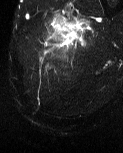
MRI of an extremity soft-tissue mass, one axial slice; position 10 of 60 along the scan axis; T2-weighted fat-saturated; MR volume resampled by the dataset authors to the PET/CT grid (not the native acquisition matrix); 3.27 mm slice thickness; 123 × 153 image matrix, field of view 120 × 149 mm. Male patient. Case-level facts recorded for this patient, not image findings: histological type: pleiomorphic liposarcoma; grade: high; site of the primary tumour: left thigh.
Outlined on this slice (expert contour drawn on MRI and transferred to this co-registered scan by the dataset authors):
- gross tumour volume including surrounding oedema: box from (x=47, y=13) to (x=91, y=44) px